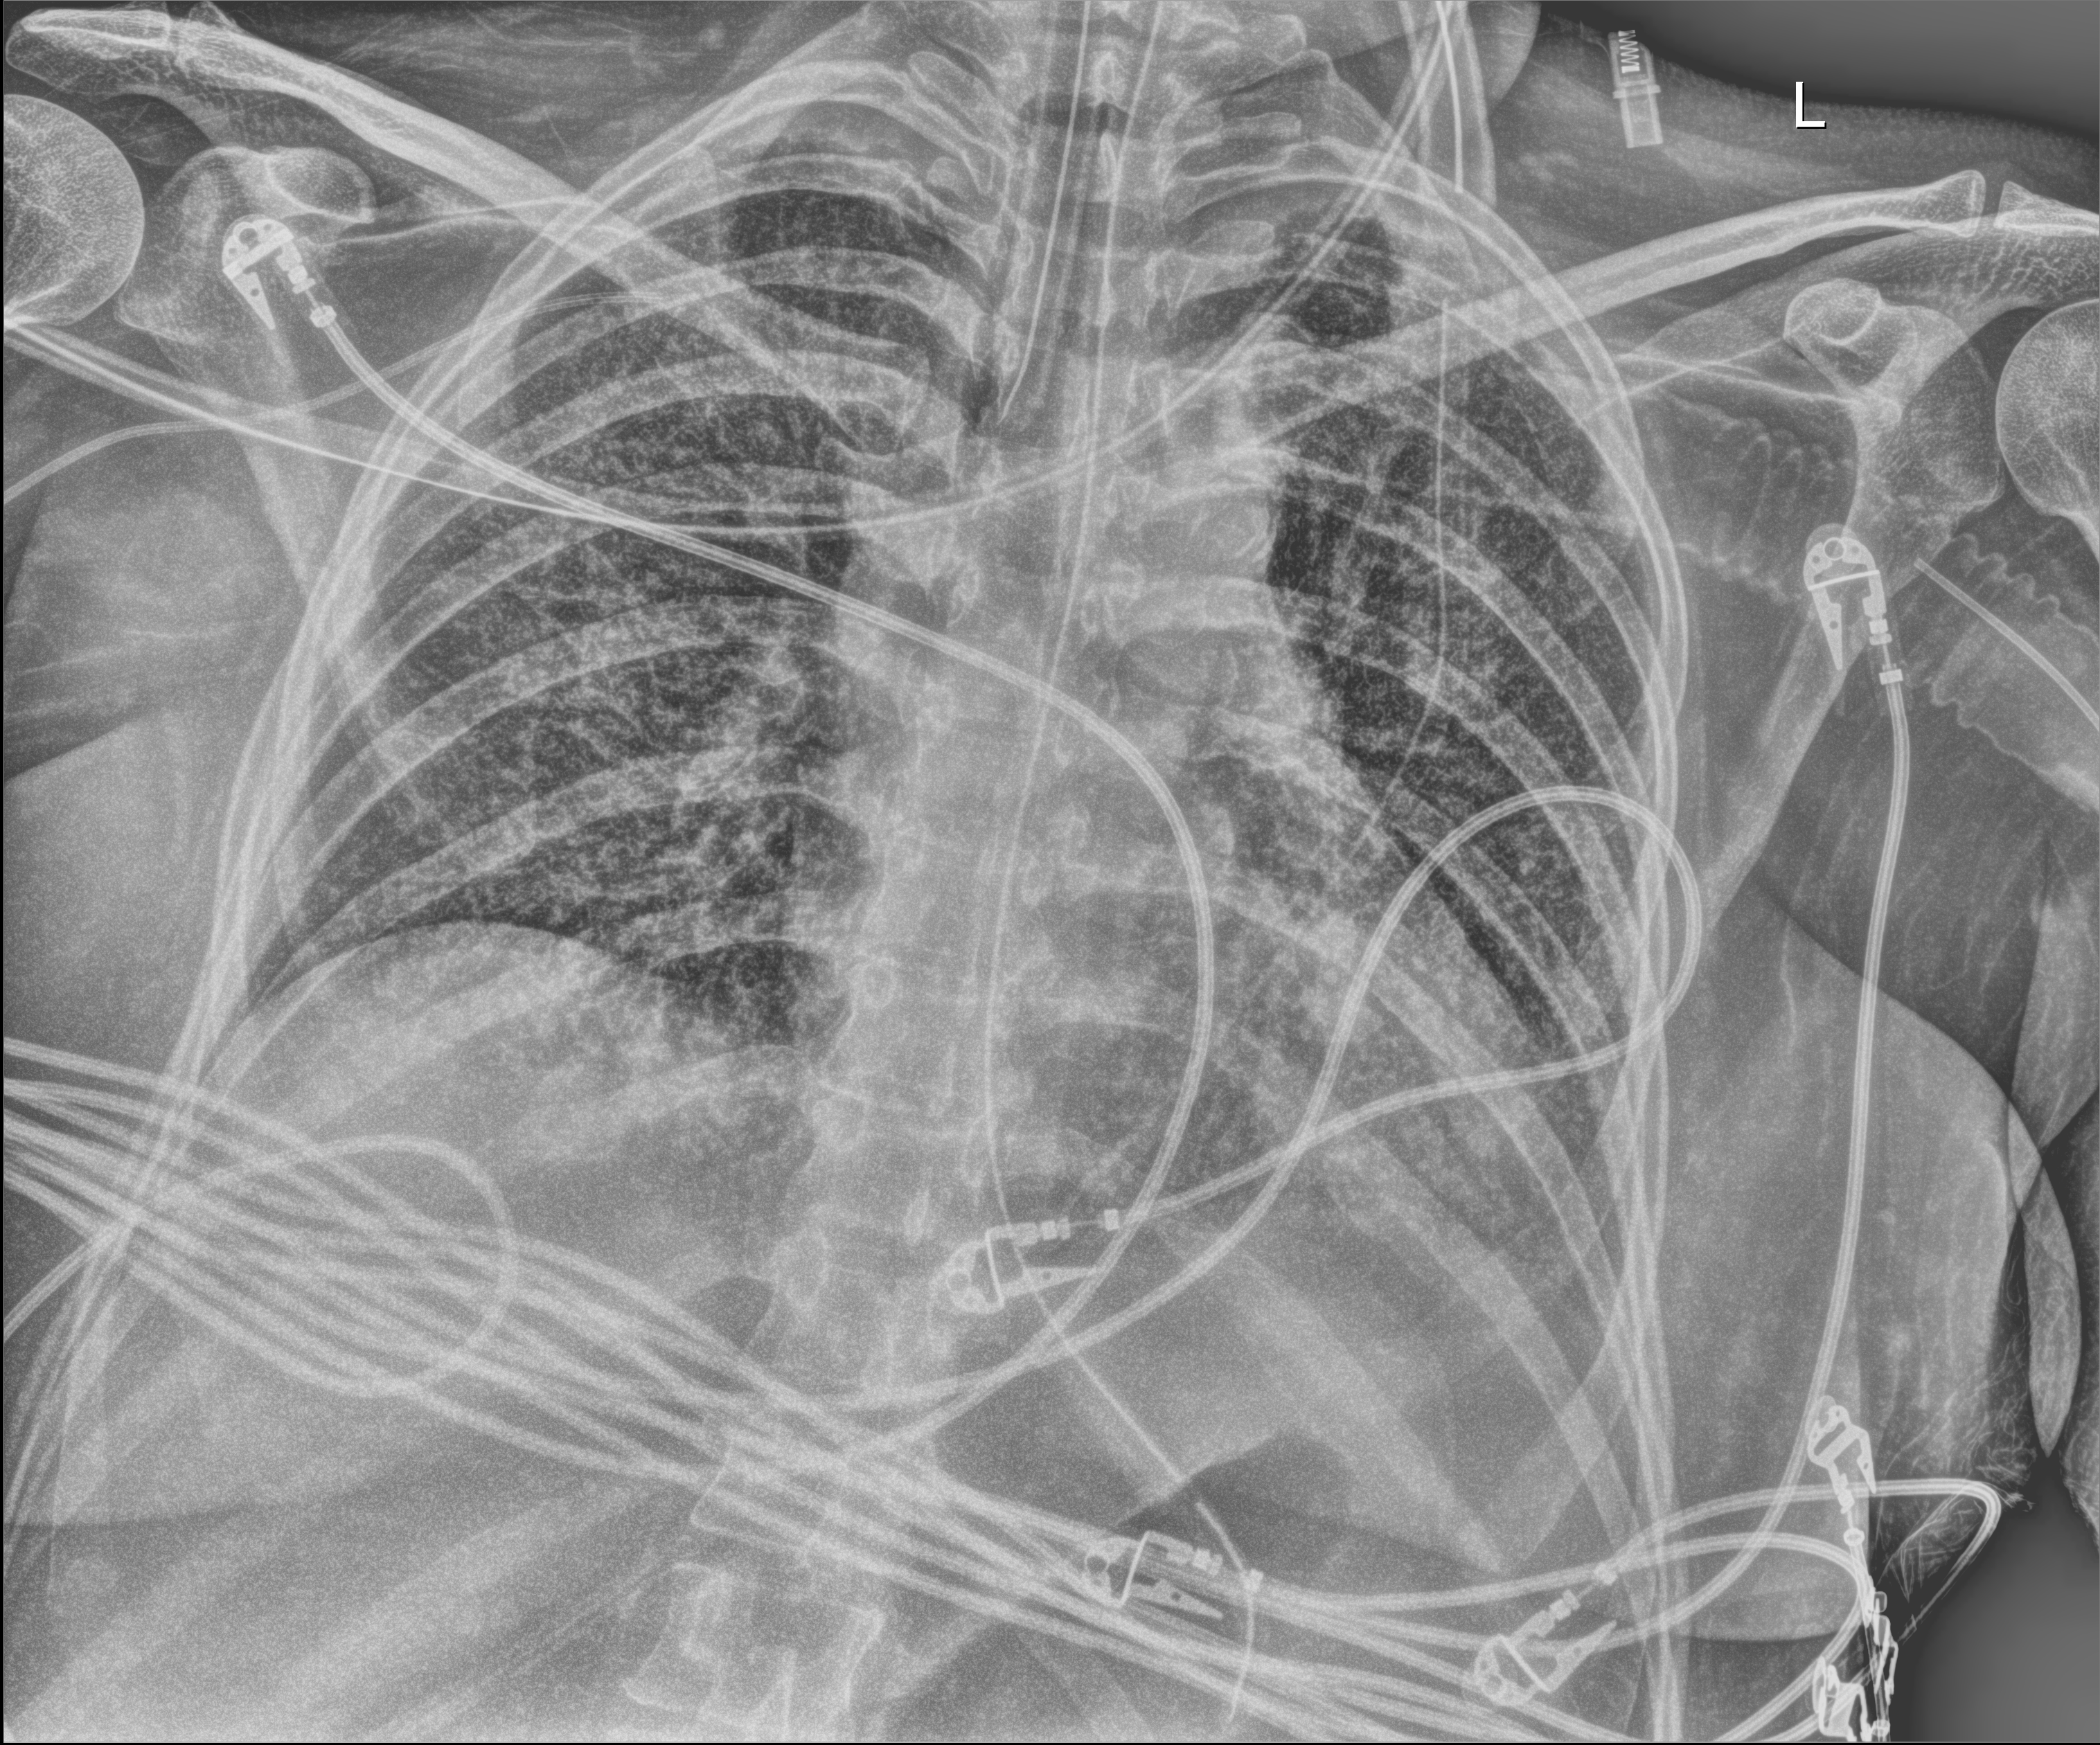
Chest radiograph (digital radiography); anteroposterior (AP) projection. Female patient hospitalised with COVID-19, age 18–59 years.
Hospital-stay facts (about this admission, not read from this image; timing relative to this image not recorded): admitted to intensive care during this hospital stay: yes; mechanically ventilated during this hospital stay: yes.